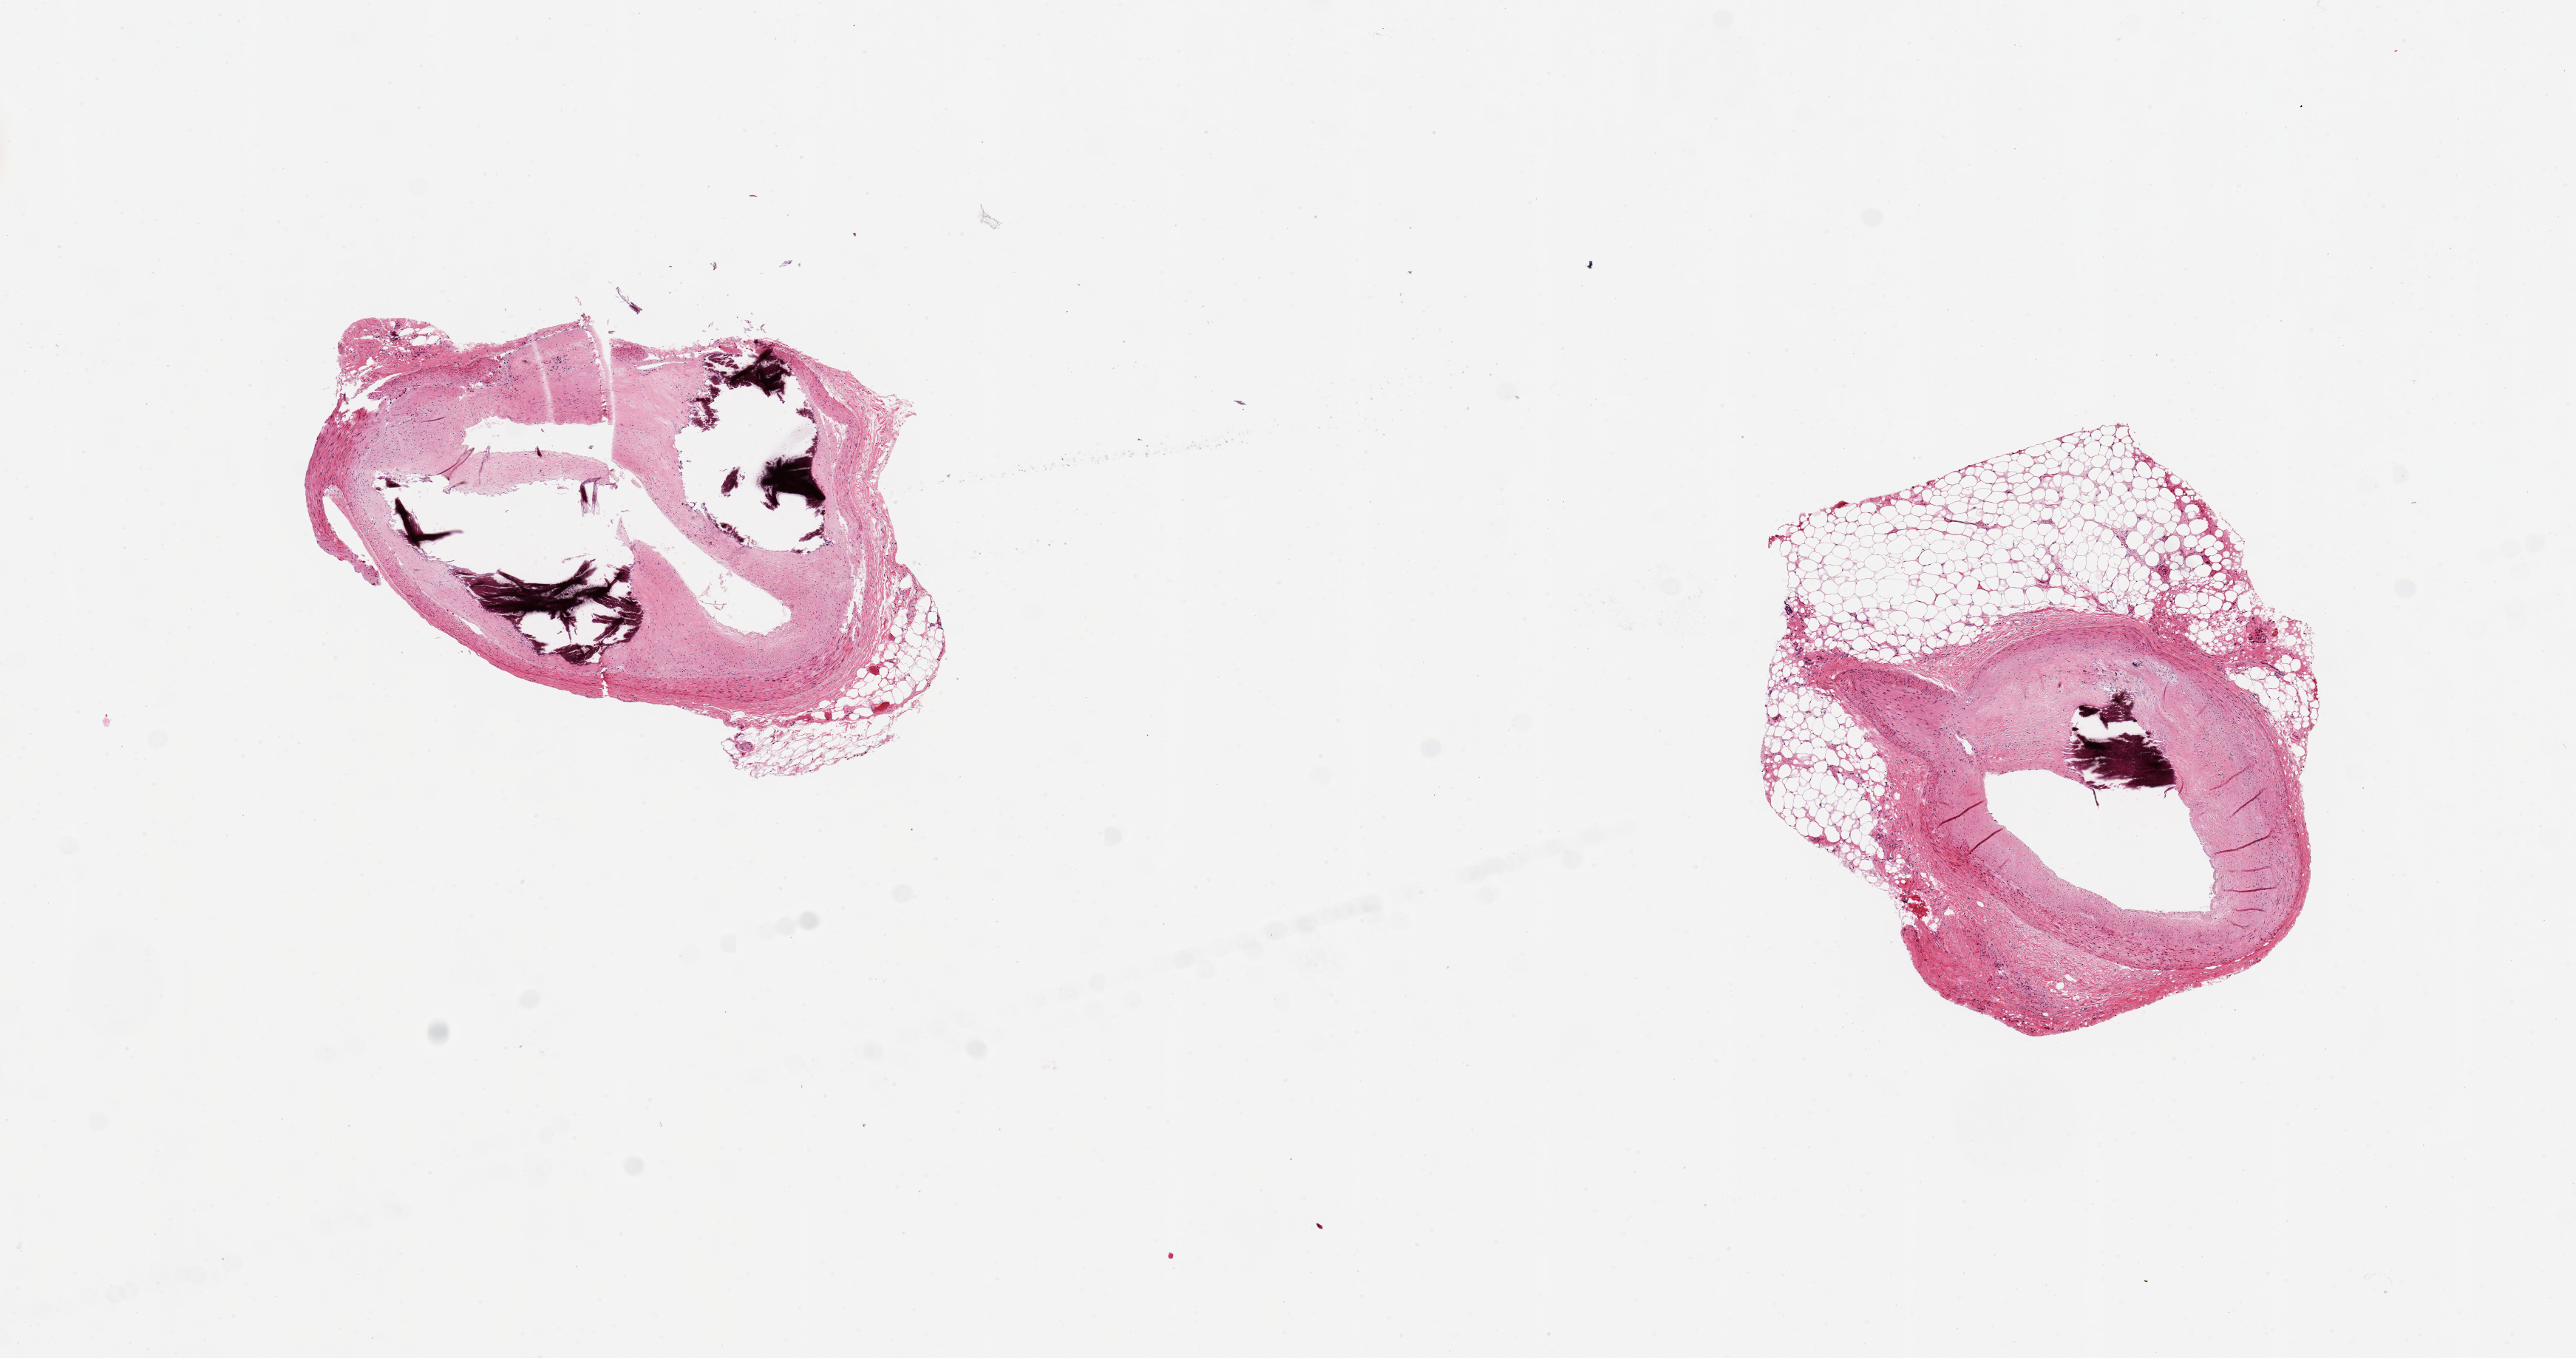
Digitized H&E-stained section, brightfield — whole scanned area (about 13.8 x 7.3 mm, slide scanned at 20x) shown as a low-resolution overview; PAXgene-fixed paraffin-embedded (PFPE) section; section of coronary artery (target tissue); tissue donor sample. Donor sex: male.
• review note (as recorded): 2 aliquots, ~2mm d. Both with subtotally occlusive calcified atherosclerosis, one with adherent ~2.5x1mm